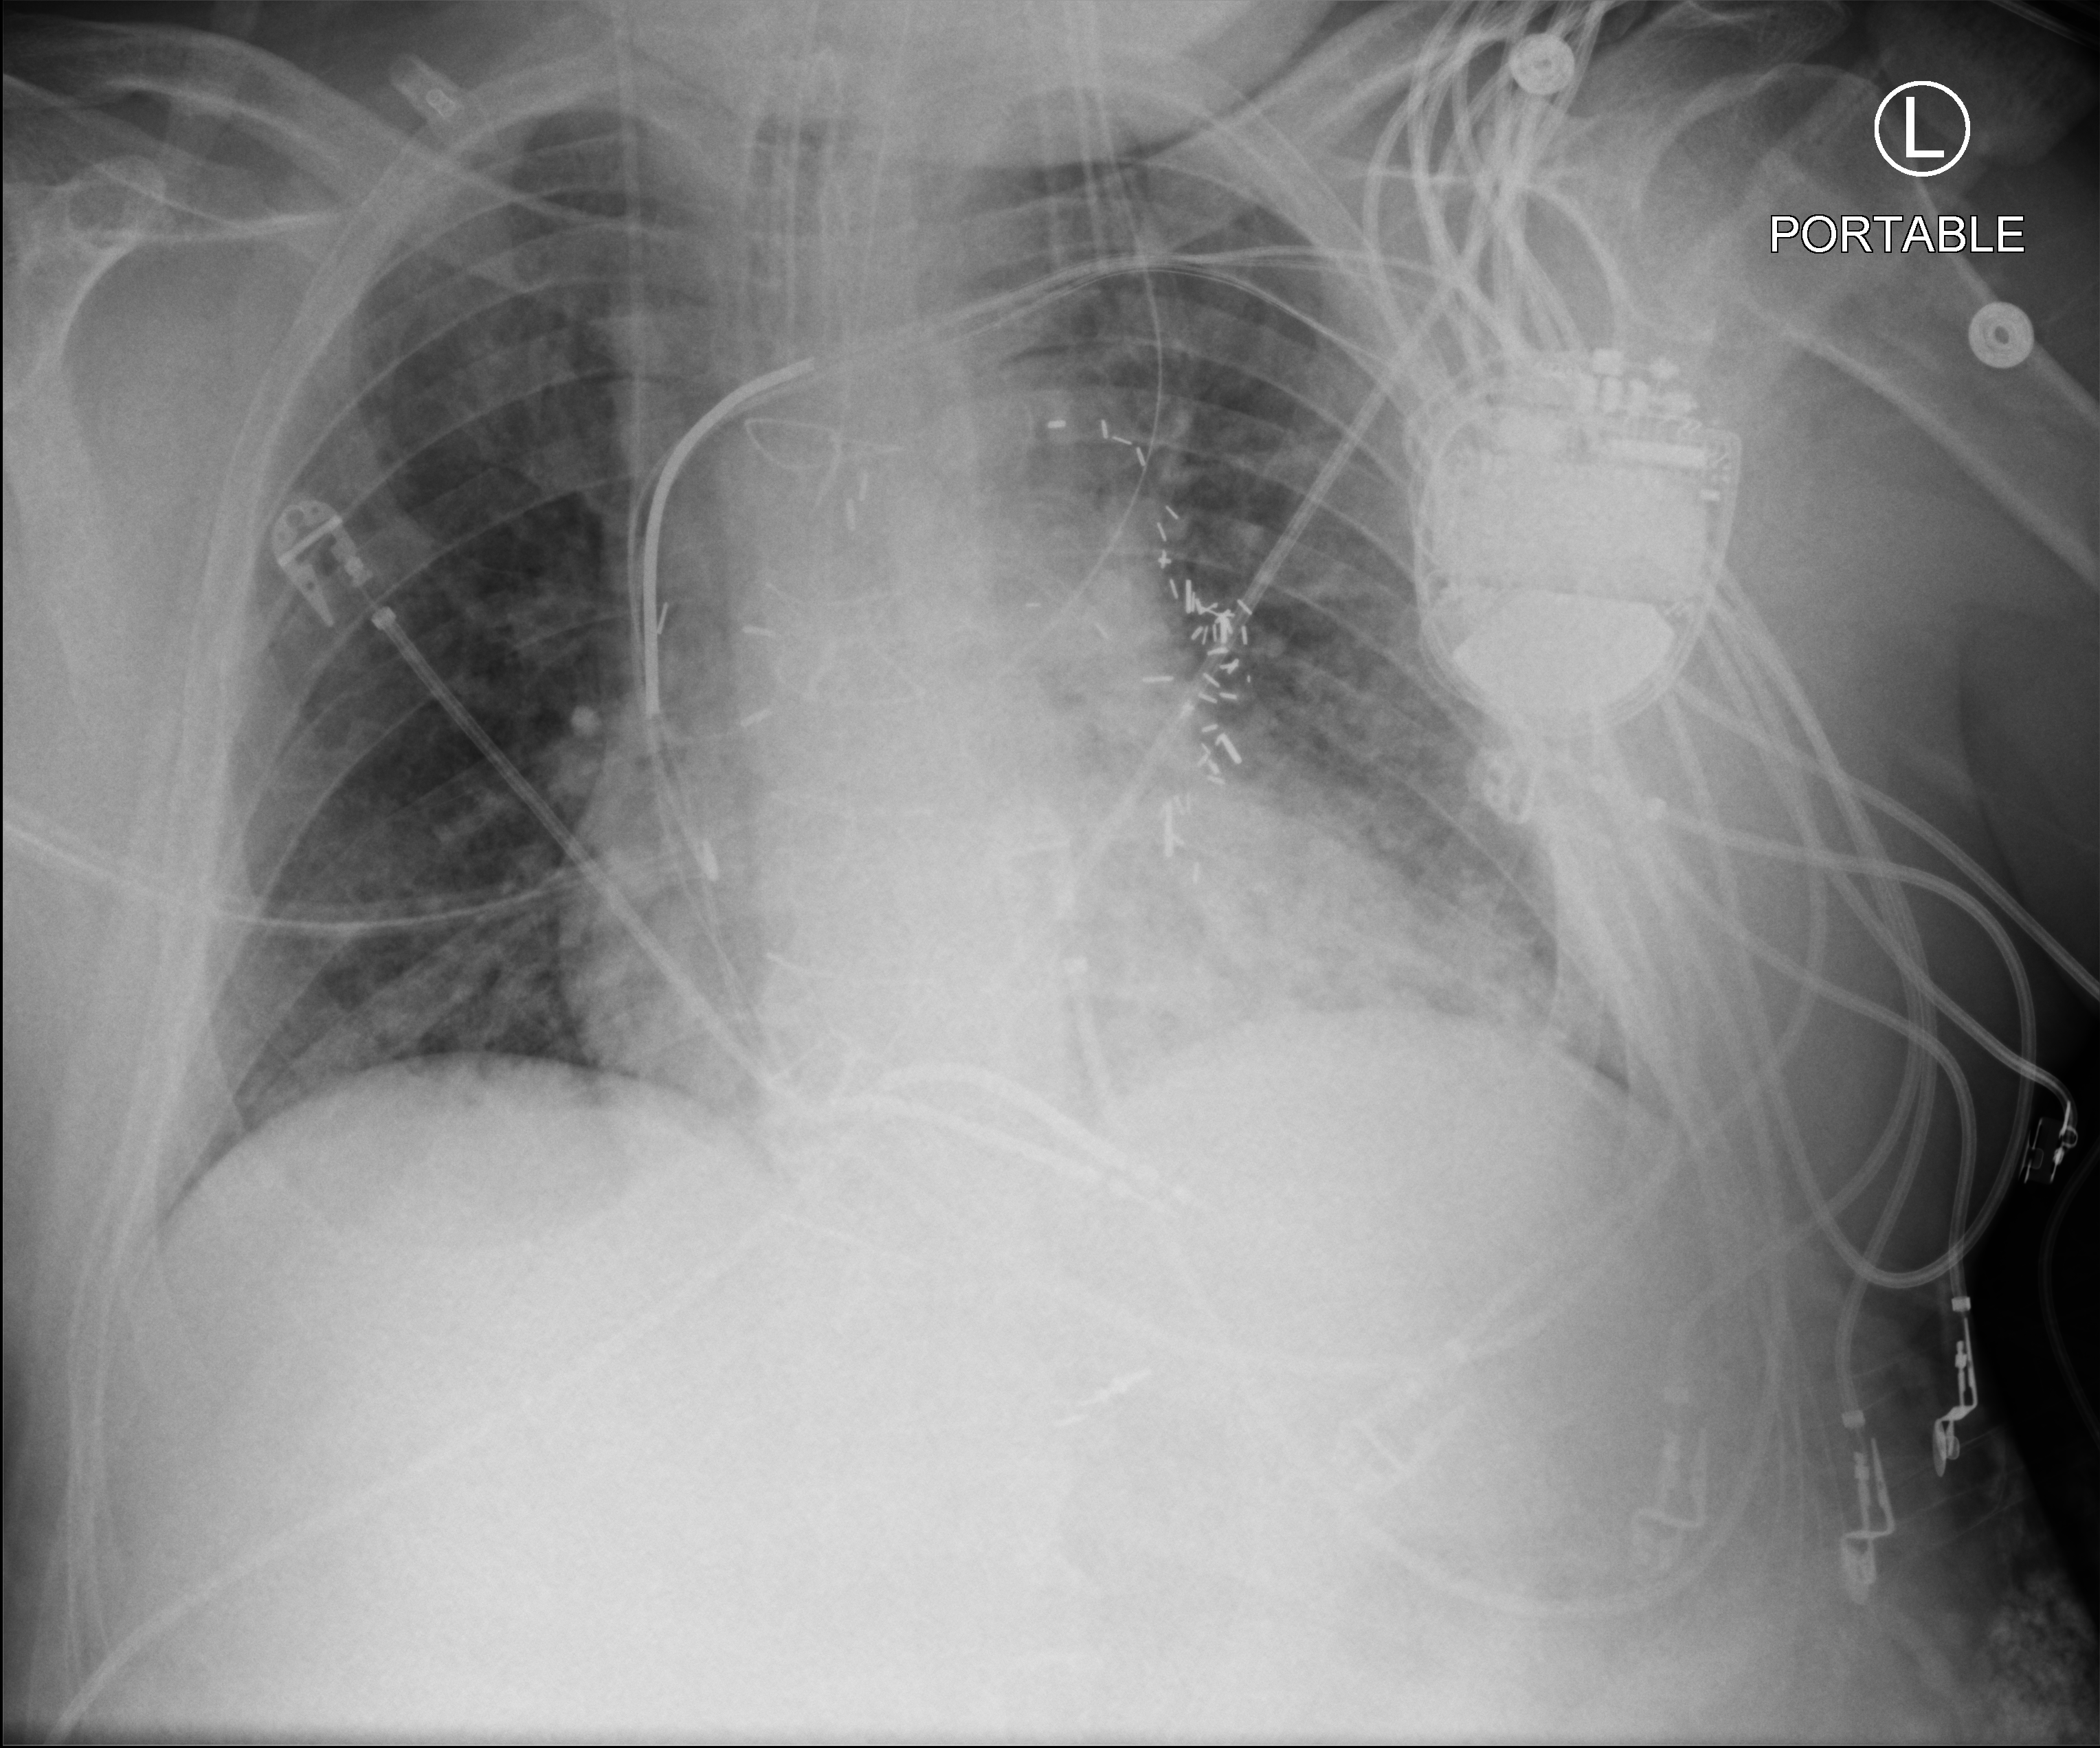
Chest X-ray (portable). Male patient hospitalised with COVID-19, age 60–74 years.
Hospital-stay facts (about this admission, not read from this image; timing relative to this image not recorded):
- mechanically ventilated during this hospital stay: yes
- admitted to intensive care during this hospital stay: yes
- diabetes (admission record): yes